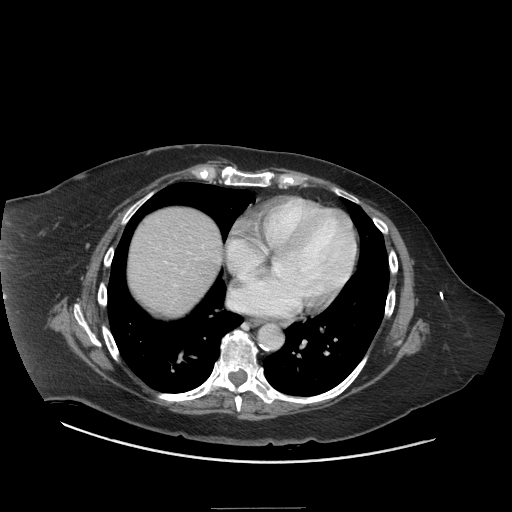
Contrast-enhanced abdominal CT (liver protocol), one axial slice; slice 71 of 81 in the series (ordered by position); soft-tissue window (W 400 / L 40 HU); 2.5 mm slice thickness; 512 × 512 image matrix, field of view 440 × 440 mm. Case-level facts recorded for this patient, not image findings: diagnosis: hepatocellular carcinoma (patient treated with transarterial chemoembolisation; whether this scan precedes or follows treatment is not stated here); TNM stage (as recorded): Stage-II; Child-Pugh class: A.
Annotated regions visible in this slice (semi-automatic segmentation, software-assisted and operator-edited):
- liver parenchyma outside the tumour (the mass and vessels are separate outlines, so this box may not span the whole liver): bounding box <128,208,220,314> (left, top, right, bottom; pixels)
- liver vessels: <156,237,204,287>